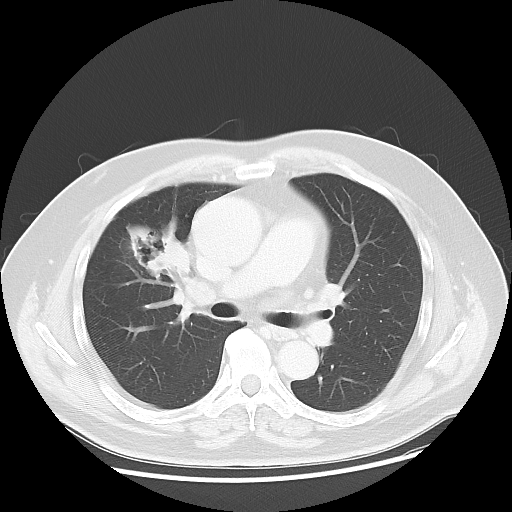
Chest CT, one axial slice; slice 26 of 48 in the series (ordered by position); reconstruction kernel LUNG; lung window (W 1500 / L -600 HU); 512 × 512 image matrix, field of view 392 × 392 mm. Male patient, age 60 years. From the clinical record (not read from this slice): clinical TNM (as recorded): T2 N3 M0.
Structures marked on this image (rectangle marked by the reading radiologist):
- lung tumour (recorded histology: adenocarcinoma): bounding box <116,214,187,301> (left, top, right, bottom; pixels)